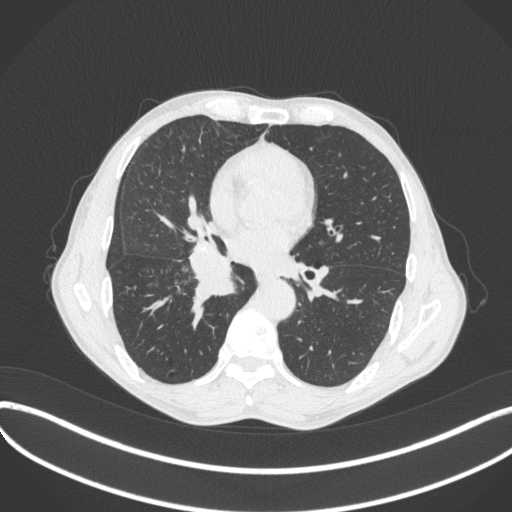
Chest CT, one axial slice. Slice 208 of 481 in the series (ordered by position). Reconstruction kernel B31f. Lung window (W 1500 / L -600 HU). 1 mm slice thickness. 512 × 512 image matrix, field of view 400 × 400 mm. Male patient, age 65 years. From the clinical record (not read from this slice): clinical TNM (as recorded): T2a N0 M0; histopathological grade: G2.
Outlined on this slice (bounding box drawn by a radiologist):
- lung tumour (recorded histology: squamous cell carcinoma): bounding box <183,240,240,306> (left, top, right, bottom; pixels)